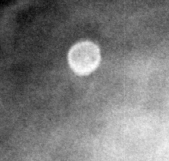
Cropped region of a digitized screen-film mammogram centred on a radiologist-marked abnormality; right breast; CC view; BI-RADS breast density category 3 (scale 1–4).
Marked abnormality: calcifications, morphology round and regular / eggshell; BI-RADS assessment category 2; benign without callback (not worked up further).